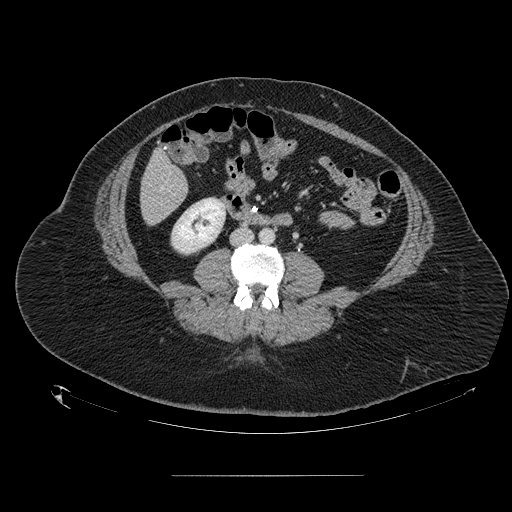
Contrast-enhanced abdominal CT, one axial slice; position 27 of 164 along the scan axis; 120 kVp; intravenous contrast given; soft-tissue window (W 400 / L 40 HU); 2.5 mm slice thickness; 512 × 512 image matrix, field of view 495 × 495 mm. Female patient, age 52 years. From the clinical record (not read from this slice): diagnosis: colorectal cancer liver metastases, imaged before liver resection; multiple liver metastases: yes; largest metastasis: 3.5 cm; disease in both lobes: no.
Outlined on this slice (expert manual segmentation):
- hepatic veins: box from (x=160, y=188) to (x=163, y=190) px
- liver: (x=142, y=152)–(x=188, y=225)